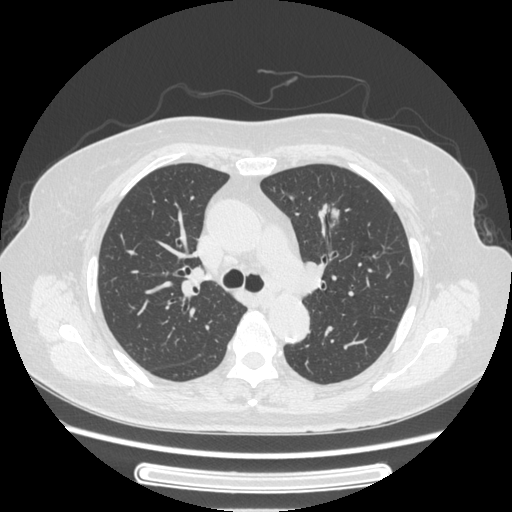
Chest CT, one axial slice; position 160 of 227 along the scan axis; lung window (W 1500 / L -600 HU); 1.25 mm slice thickness; 512 × 512 image matrix, field of view 363 × 363 mm. Patient: female, 77 years. From the clinical record (not read from this slice): clinical TNM (as recorded): T1c N3 M0.
Structures marked on this image (bounding box drawn by a radiologist):
- lung tumour (recorded histology: adenocarcinoma): bounding box [x1, y1, x2, y2] px = [310, 198, 349, 243]